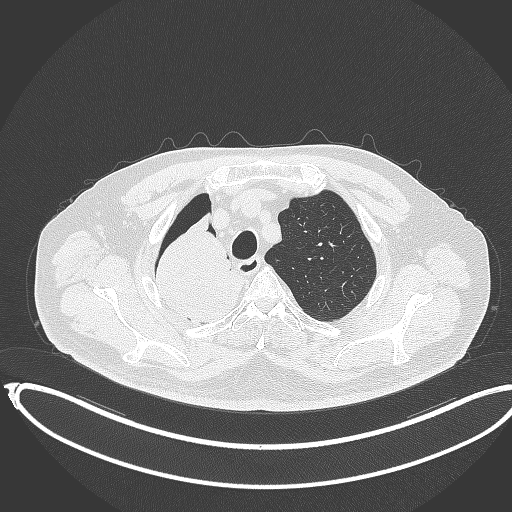
Chest CT, one axial slice; position 305 of 403 along the scan axis; reconstruction kernel B70f; lung window (W 1500 / L -600 HU); 512 × 512 image matrix. Patient: male, 68 years. From the clinical record (not read from this slice): clinical TNM (as recorded): T2a N0 M0.
Outlined on this slice (rectangle marked by the reading radiologist):
- lung tumour (recorded histology: adenocarcinoma): bounding box [x1, y1, x2, y2] px = [149, 207, 245, 325]